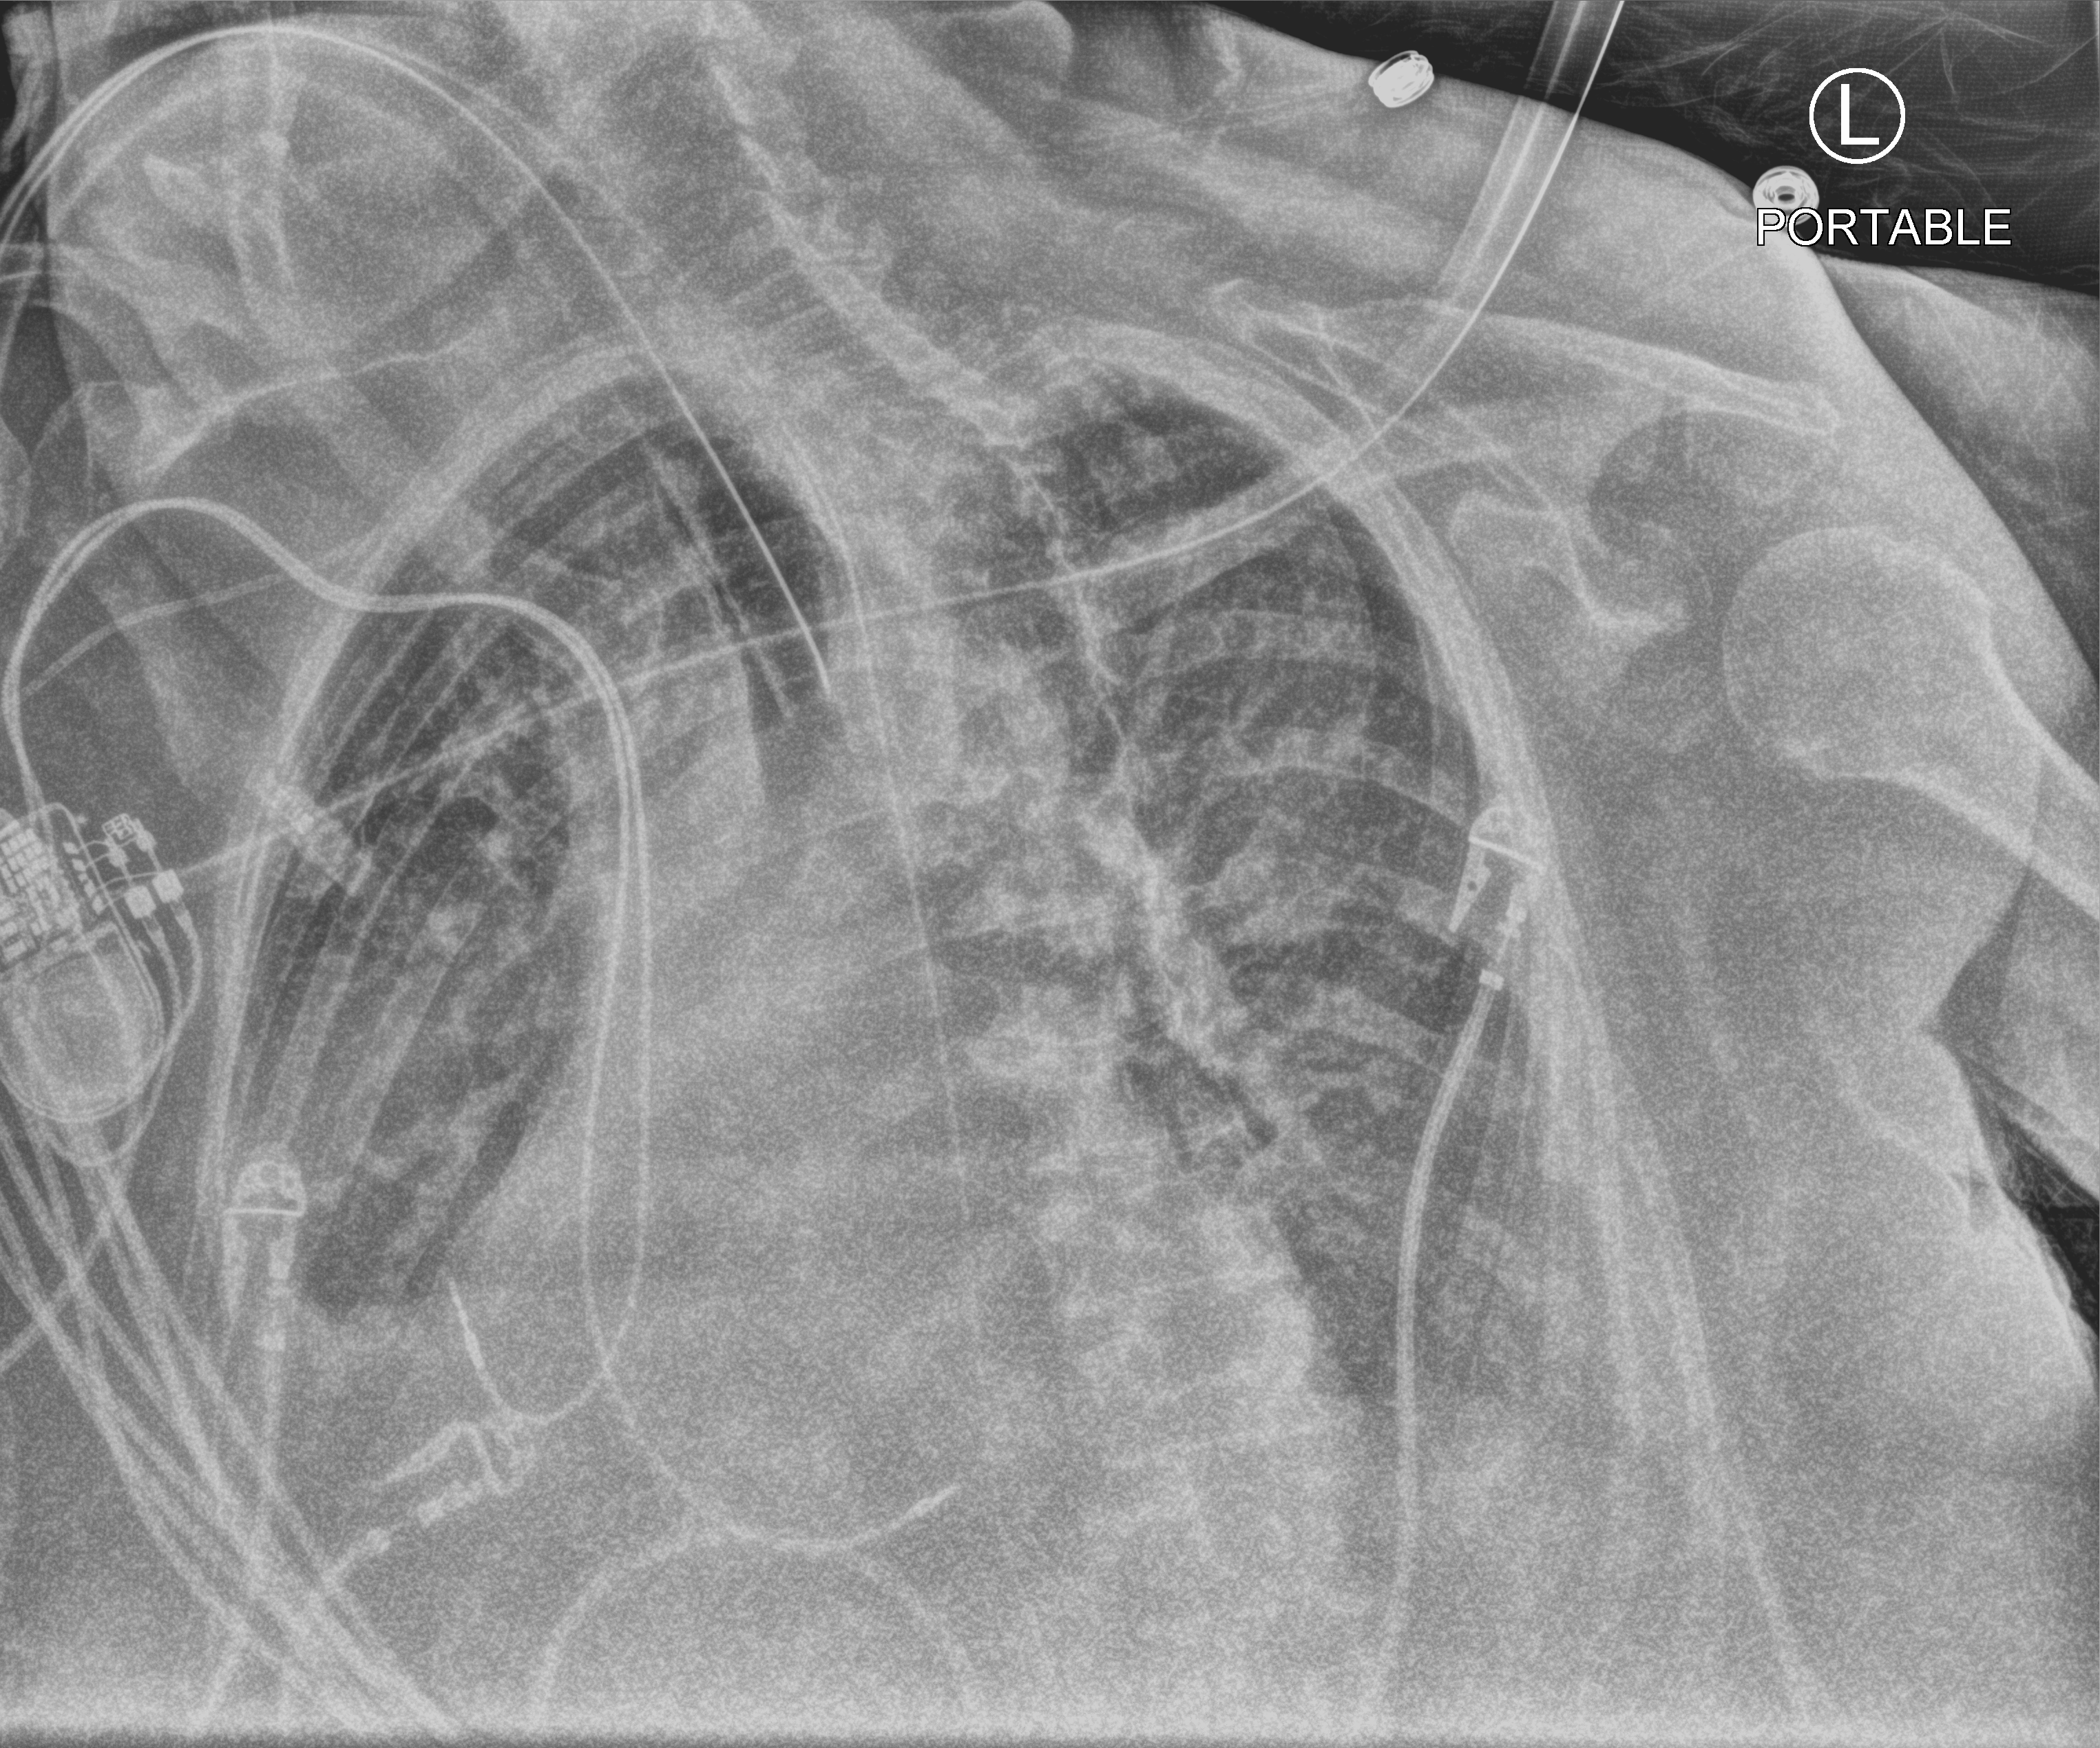
Bedside chest radiograph (computed radiography), anteroposterior (AP) projection. Female patient hospitalised with COVID-19, age 75–90 years.
Admission-level facts for this patient (not findings on this image; timing relative to this image not recorded):
- length of hospital stay: 21 days
- mechanically ventilated during this hospital stay: yes
- COPD (admission record): yes